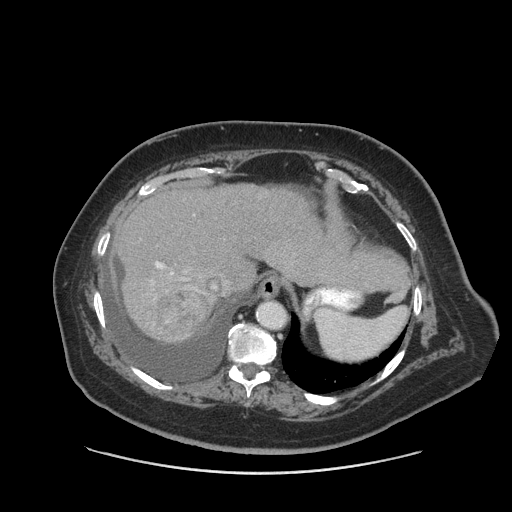
Contrast-enhanced abdominal CT (liver protocol), one axial slice; slice 67 of 91 in the series (ordered by position); reconstruction kernel STANDARD; 140 kVp; soft-tissue window (W 400 / L 40 HU); 2.5 mm slice thickness; 512 × 512 image matrix, field of view 420 × 420 mm. Case-level facts recorded for this patient, not image findings: diagnosis: hepatocellular carcinoma (patient treated with transarterial chemoembolisation; whether this scan precedes or follows treatment is not stated here); TNM stage (as recorded): Stage-I; Child-Pugh class: A; tumour nodularity: uninodular.
Outlined on this slice (semi-automatically segmented with operator editing):
- liver parenchyma outside the tumour (the mass and vessels are separate outlines, so this box may not span the whole liver): bounding box (x1, y1, x2, y2) in pixels: (114, 184, 334, 342)
- mass: (145, 290, 209, 340)
- liver vessels: (155, 262, 215, 288)